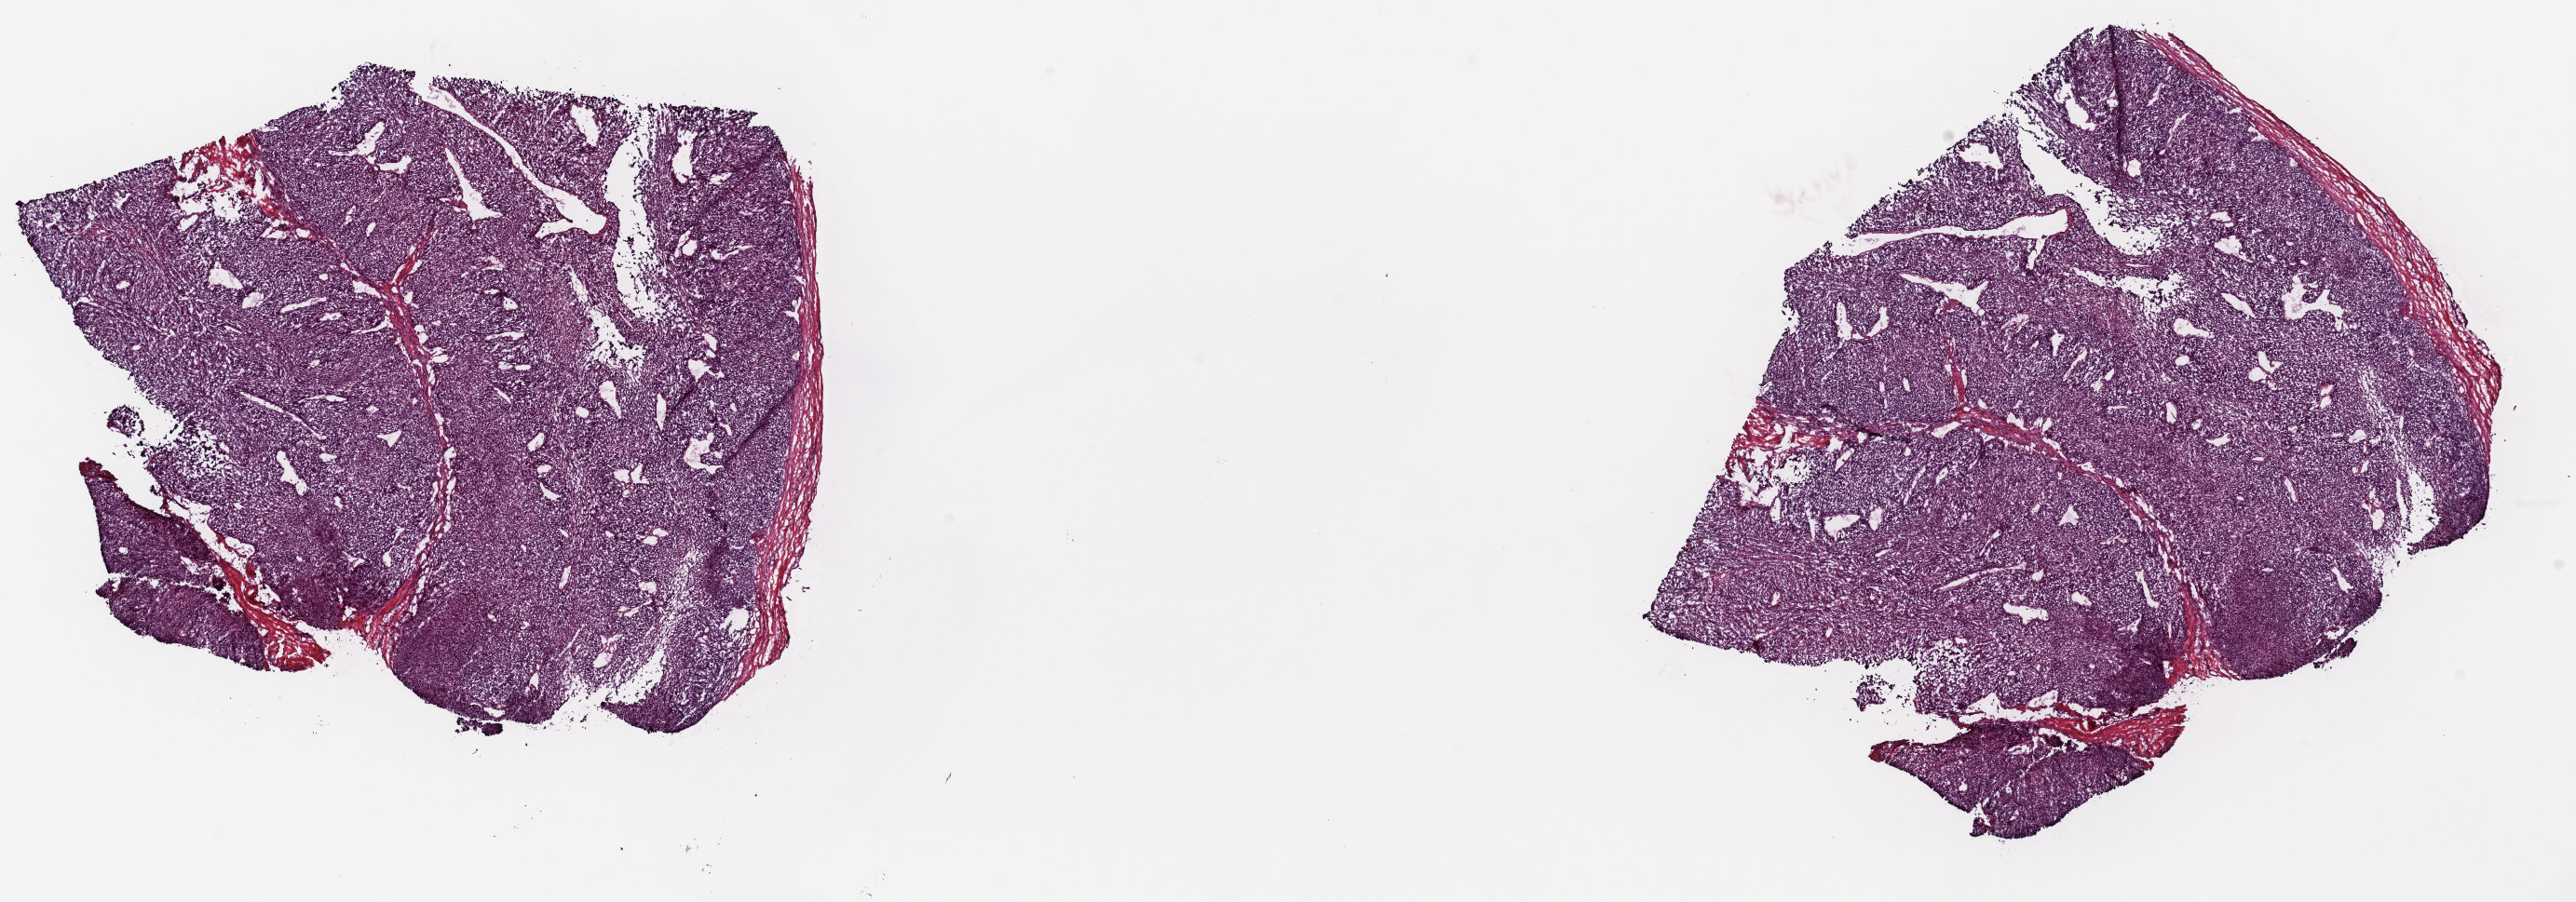
Whole-slide histology image, H&E-stained, a low-resolution overview of the entire scanned area, about 21.8 x 7.6 mm. Frozen section from the top of the tissue portion. Metastatic tumour sample, sampled site: lymph node. Male patient; age at initial diagnosis 60 years. Pathologist review of this section (percent, as recorded): tumour cells 85%, tumour nuclei 85%, normal cells 0%, stromal cells 15%, necrosis 0%. Inflammatory infiltration, as recorded: lymphocyte infiltration 2%, monocyte infiltration 0%, neutrophil infiltration 0%.
This section: metastatic tumour tissue. Patient diagnosis: Malignant melanoma, NOS.